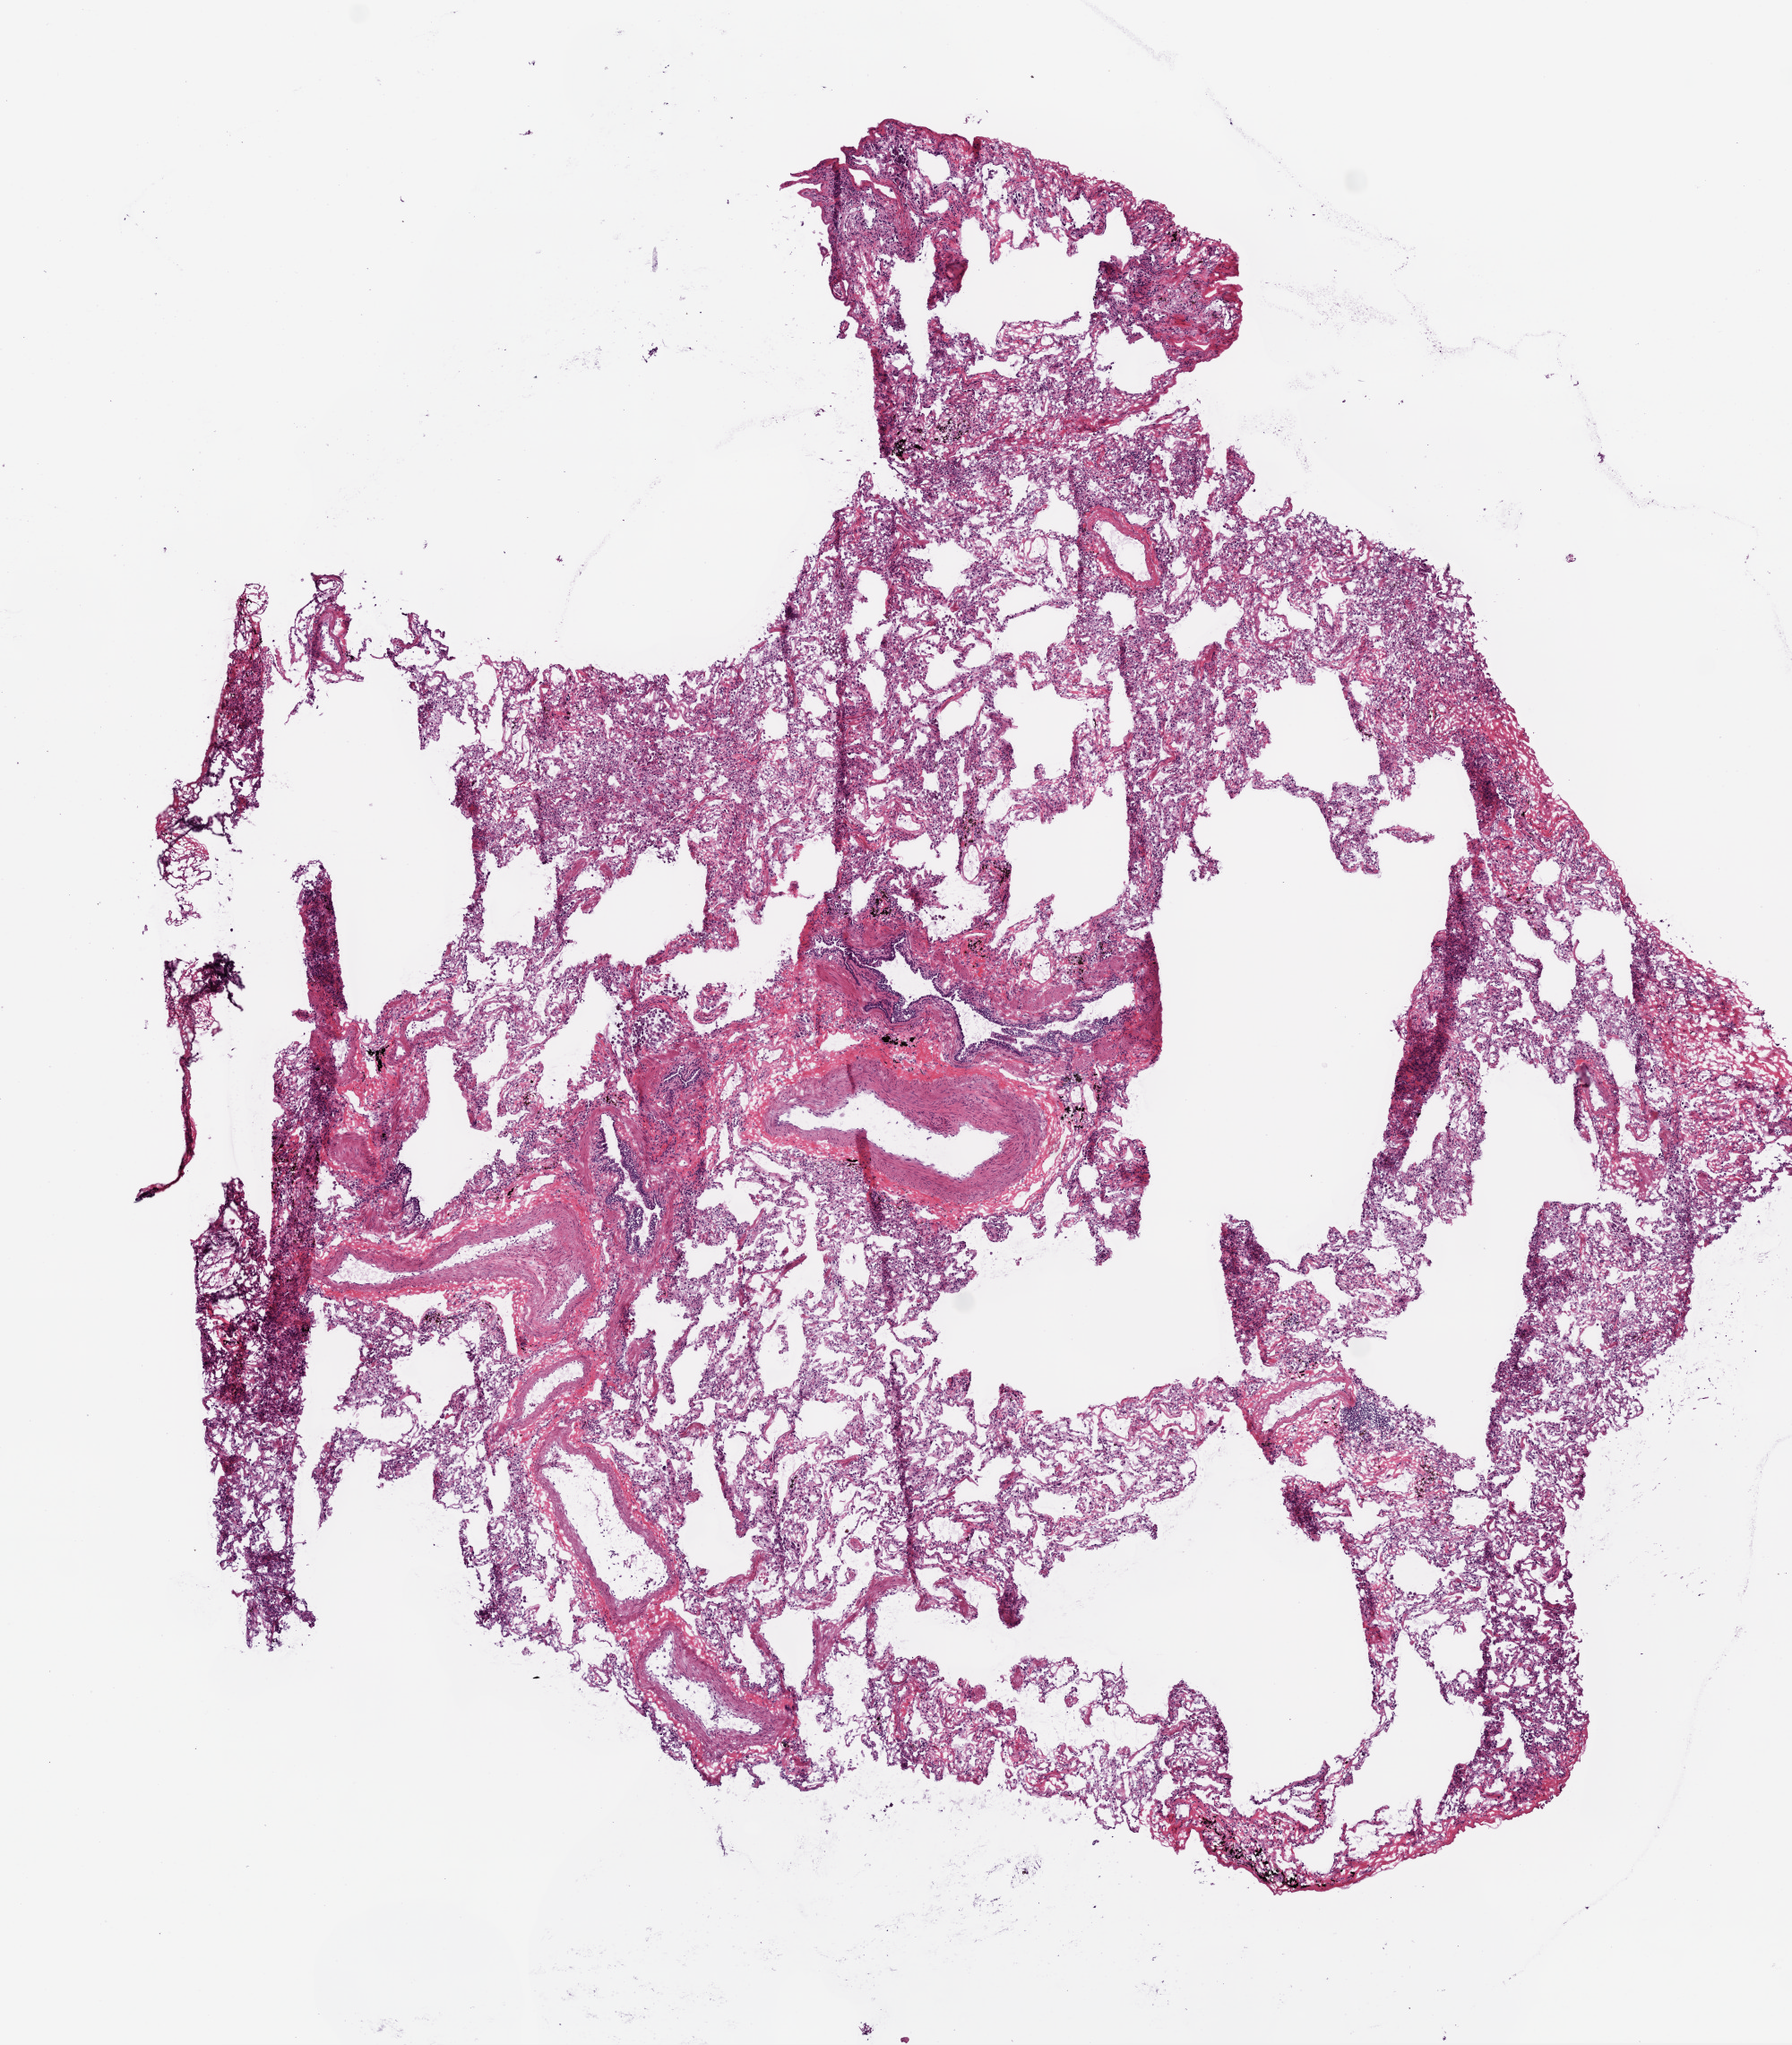
Whole-slide histology image, Hematoxylin and eosin (H&E) stained — low-resolution overview of the scanned area, about 8.0 x 9.2 mm, frozen section from the top of the tissue portion, lung, solid tissue normal (non-tumour tissue) sample. Patient: female, age at initial diagnosis 73 years.
This section: solid tissue normal sample (biorepository sample class). Patient diagnosis: Squamous cell carcinoma, NOS (upper lobe, lung).